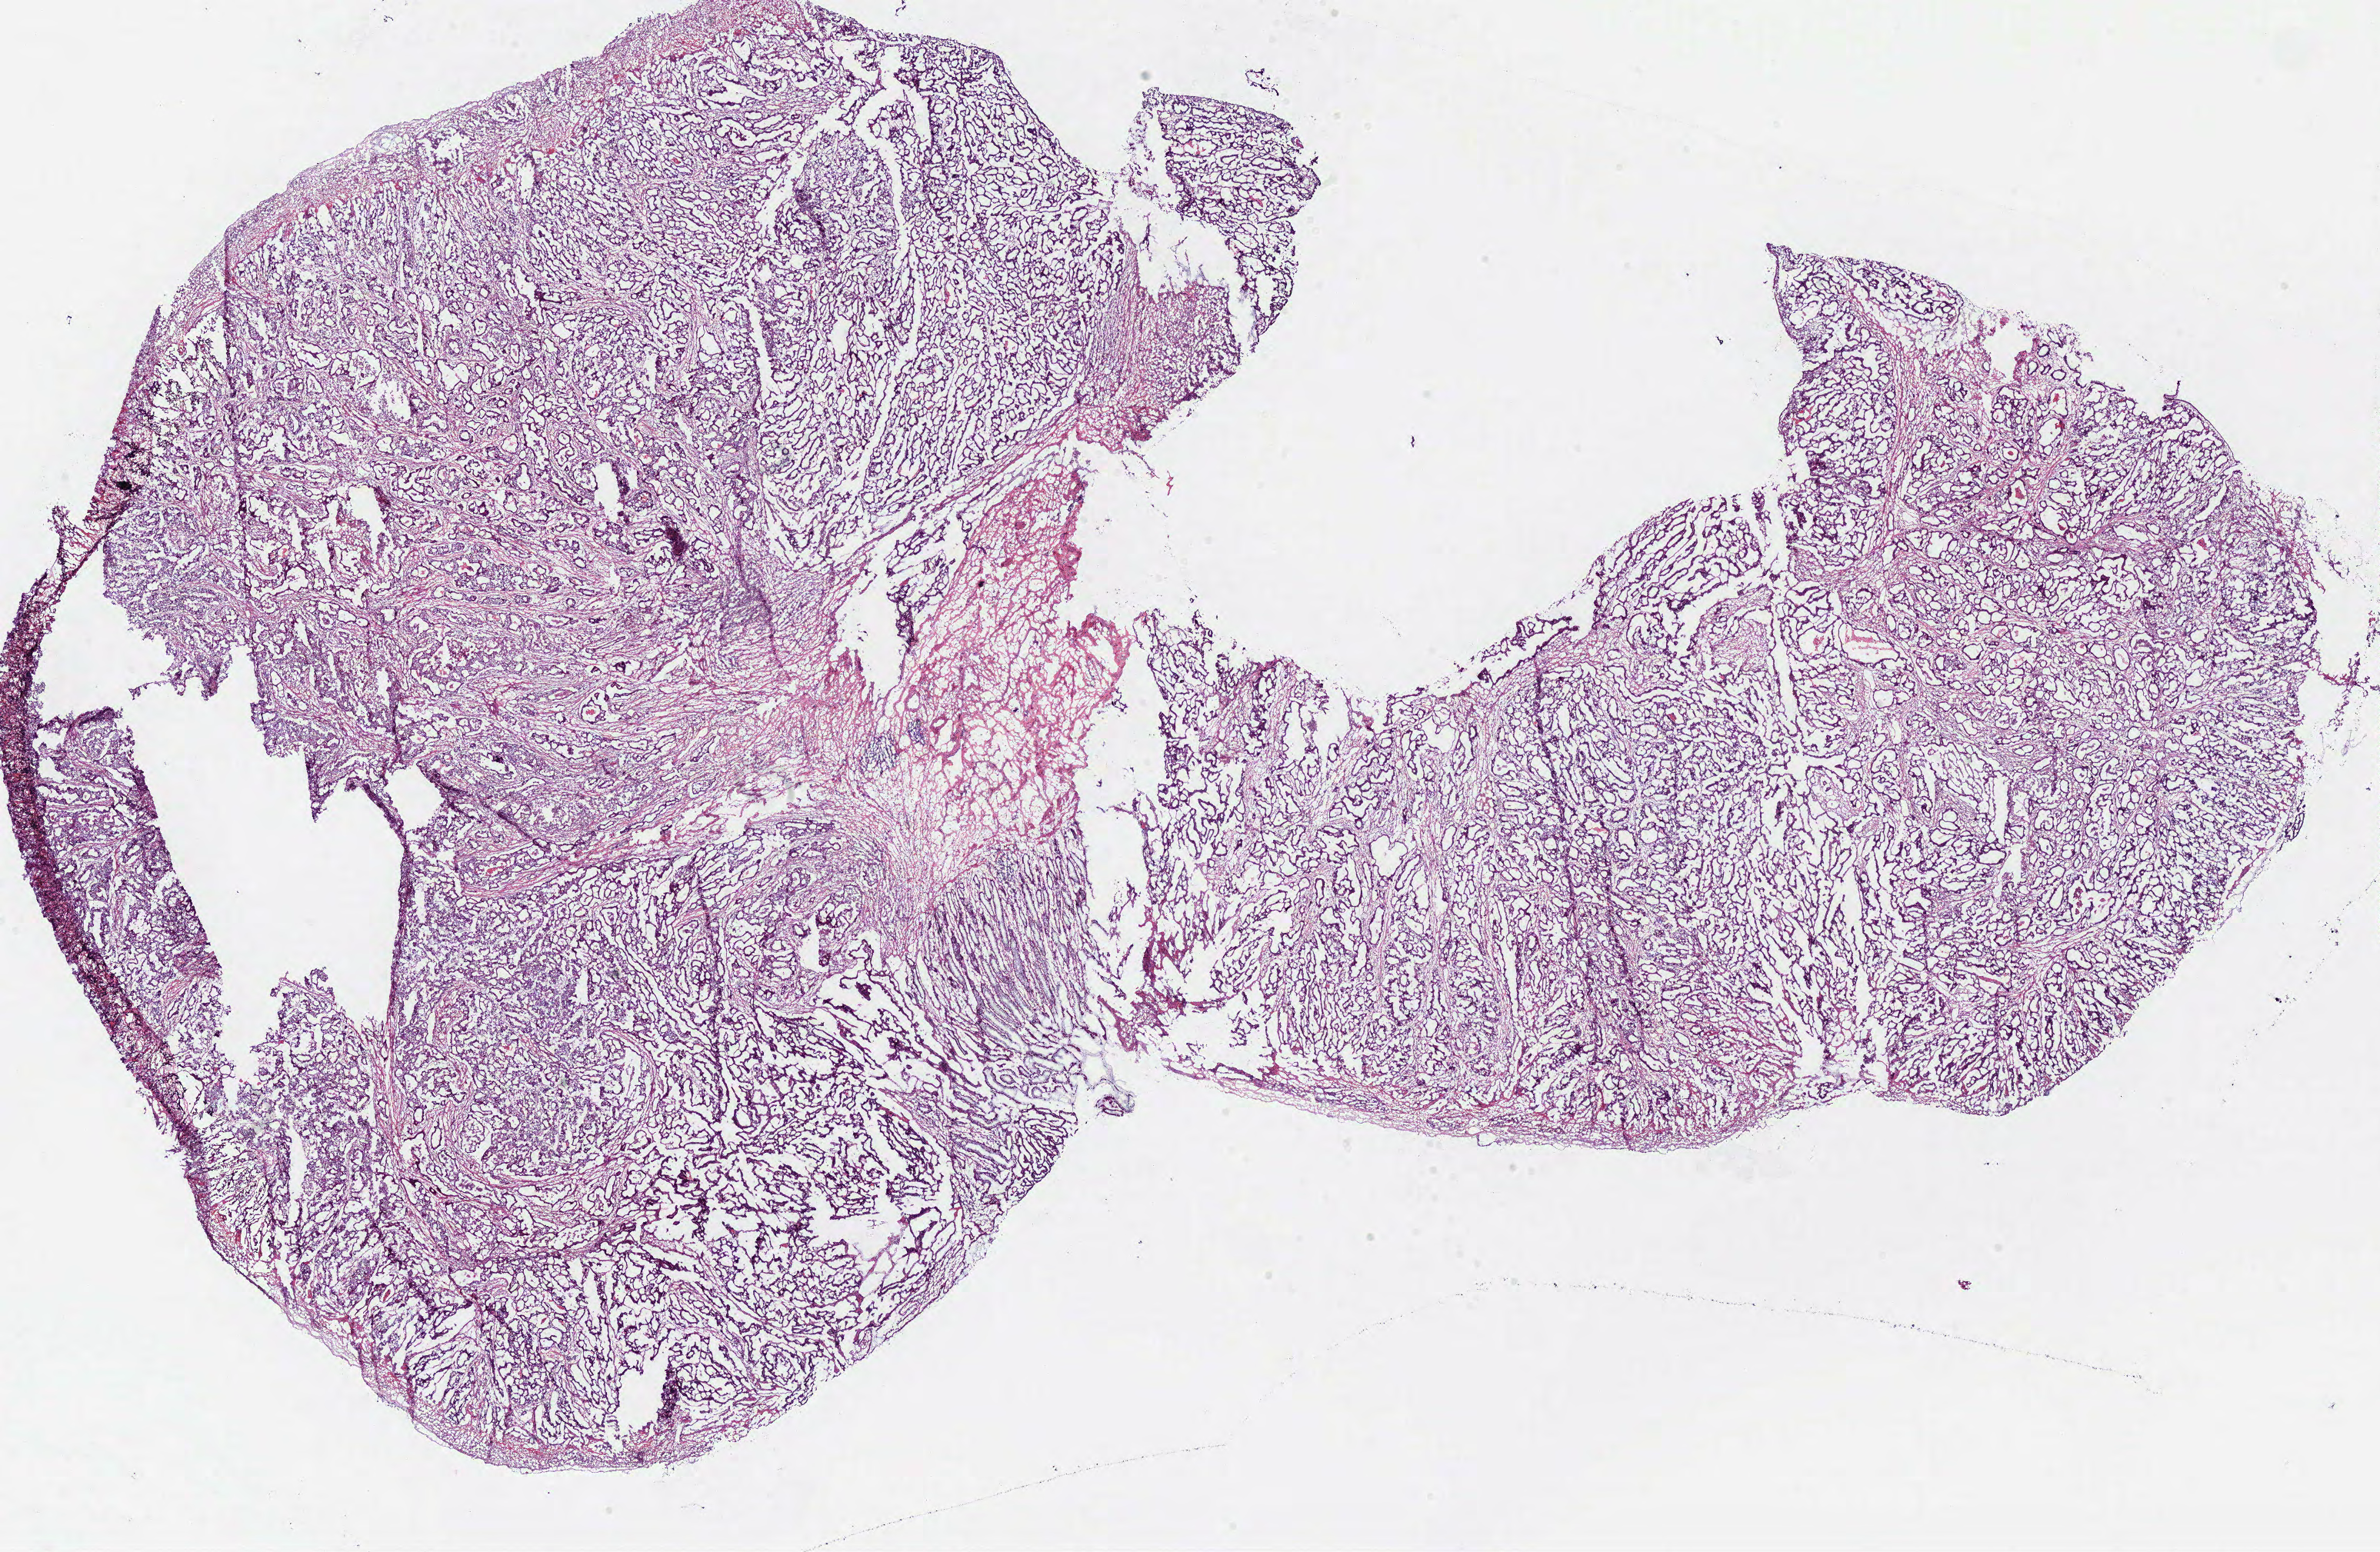
Whole-slide histology image, H&E-stained — whole scanned area (about 24.4 x 15.9 mm) shown as a low-resolution overview; frozen section; colon, primary tumour sample. Female, age 54 years at initial diagnosis.
Histologic diagnosis: Adenocarcinoma, NOS (sigmoid colon).